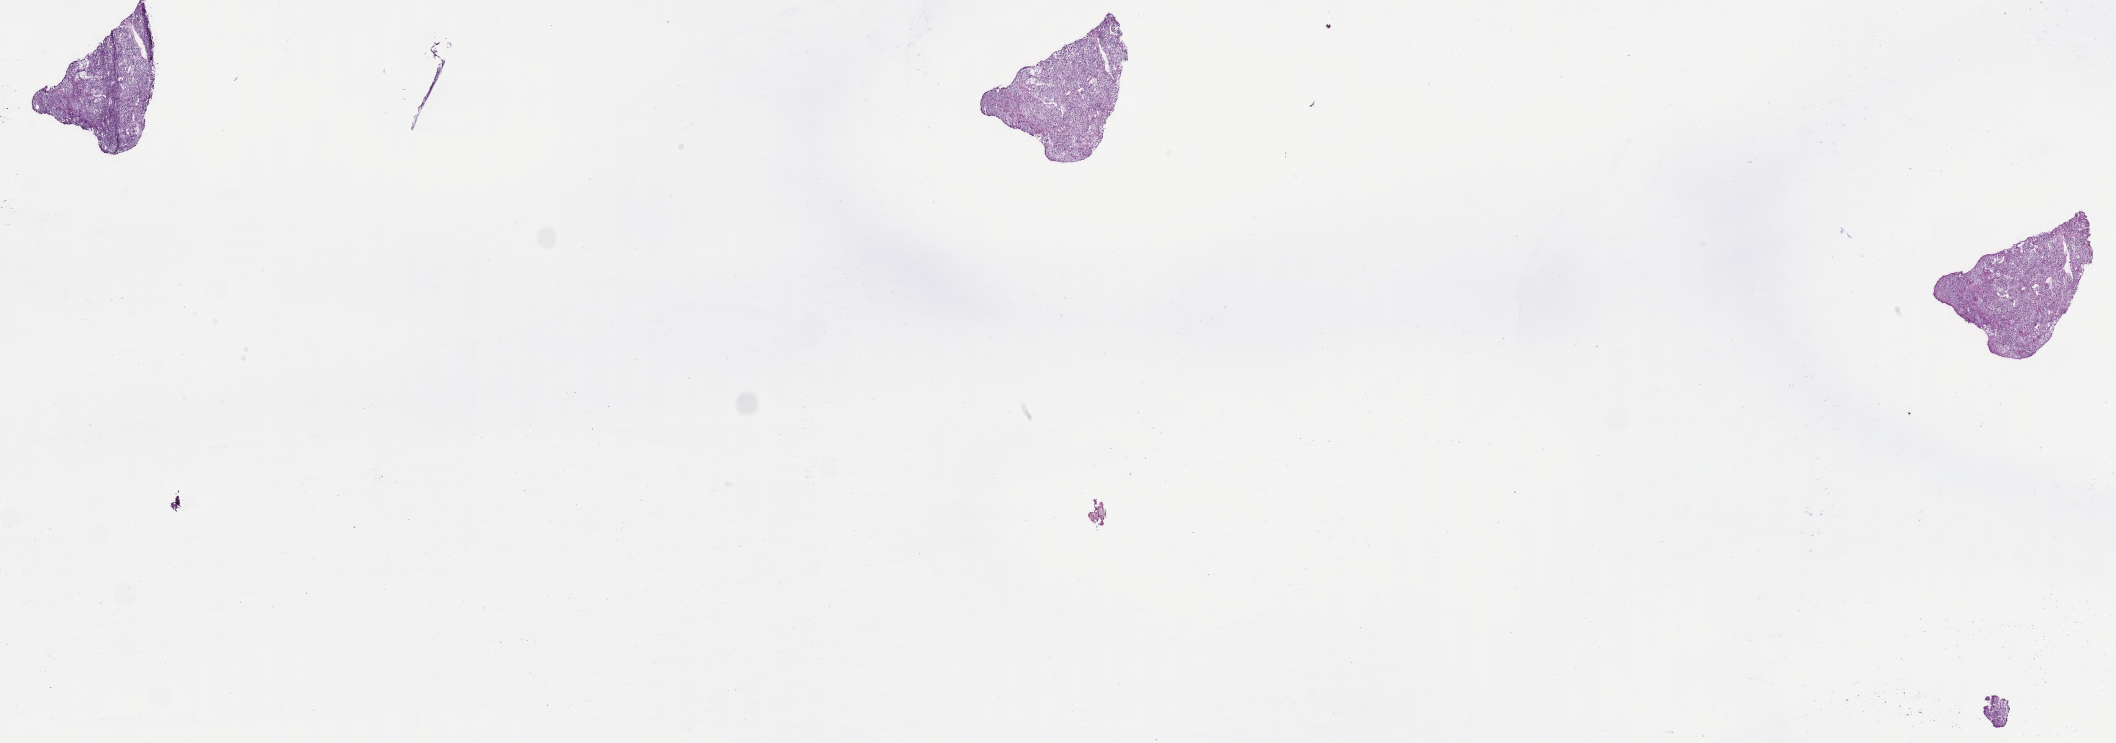
Whole-slide image, hematoxylin and eosin (H&E) stain of tumor tissue from the adrenal gland, low-resolution overview of the scanned area, about 34.2 x 12.0 mm. Frozen section (OCT-embedded). Male patient, age 133 months (11 years 1 month).
• diagnosis: Pheochromocytoma, NOS